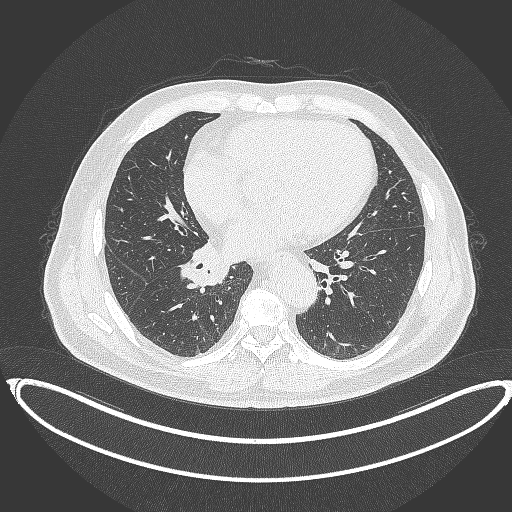
Chest CT, one axial slice. Slice 174 of 387 in the series (ordered by position). Reconstruction kernel B70f. 120 kVp. Lung window (W 1500 / L -600 HU). 512 × 512 image matrix, field of view 448 × 448 mm. Male patient, age 61 years. Case-level facts recorded for this patient, not image findings: clinical TNM (as recorded): T1b N1 M0.
Structures marked on this image (bounding box drawn by a radiologist):
- lung tumour (recorded histology: squamous cell carcinoma): box from (x=174, y=240) to (x=227, y=293) px